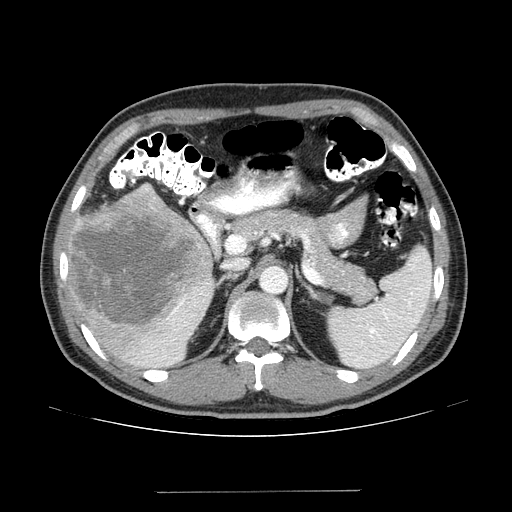
Contrast-enhanced abdominal CT (liver protocol), one axial slice. Slice 80 of 131 in the series (ordered by position). Reconstruction kernel STANDARD. 100 kVp. One of 2 acquisitions stored at this slice position. Soft-tissue window (W 400 / L 40 HU). 512 × 512 image matrix. Case-level facts recorded for this patient, not image findings: diagnosis: hepatocellular carcinoma (patient treated with transarterial chemoembolisation; whether this scan precedes or follows treatment is not stated here); TNM stage (as recorded): Stage-I; Child-Pugh class: A.
Outlined on this slice (semi-automatically segmented with operator editing):
- liver parenchyma outside the tumour (the mass and vessels are separate outlines, so this box may not span the whole liver): bounding box [x1, y1, x2, y2] px = [66, 184, 217, 368]
- mass: [68, 187, 211, 333]
- liver vessels: [151, 239, 215, 358]